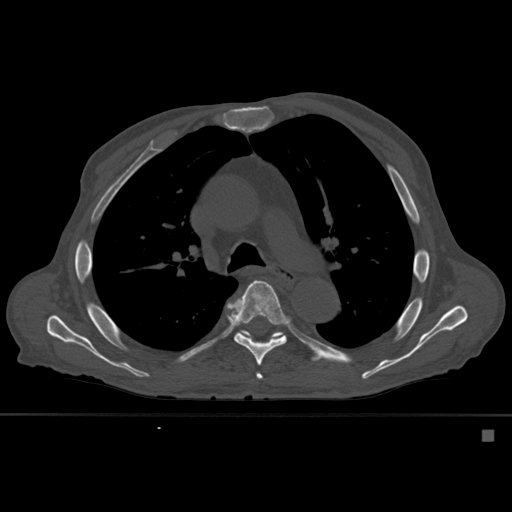
CT including the spine, one axial slice; position 383 of 527 along the scan axis; bone window (W 1800 / L 400 HU); 512 × 512 image matrix, field of view 373 × 373 mm. Patient: male, 78 years. Case-level facts recorded for this patient, not image findings: primary cancer: prostate.
Outlined on this slice (semi-automatic segmentation, software-assisted and operator-edited):
- T5 vertebra: bounding box <256,373,263,380> (left, top, right, bottom; pixels)
- T6 vertebra: <225,280,291,366>
- T7 vertebra: <240,330,284,339>